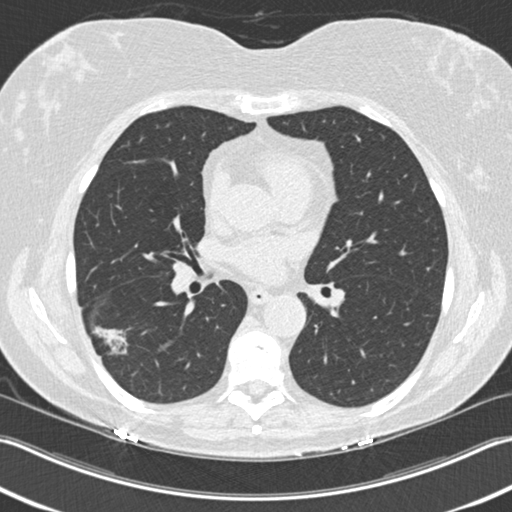
Chest CT (low-dose screening protocol), one axial image, baseline annual screen, lung window (W 1500 / L -600 HU), 2 mm slice thickness, standard (soft-tissue) reconstruction kernel (B30f), 120 kVp, slice 92 of 211 in the series. Female participant, aged 63 years at enrolment. Current smoker at enrolment.
Expert reader's lesion annotation, bounding box <82,317,142,371> (left, top, right, bottom; pixels). The screening reader recorded 3 non-calcified nodules or masses ≥4 mm on this exam (right upper lobe, right lower lobe, right lower lobe); which of them this box marks is not recorded. Official screen result: positive, change unspecified: nodule(s) >= 4 mm or enlarging nodule(s), mass(es), or other non-specific abnormalities suspicious for lung cancer. Later outcome: lung cancer diagnosed 57 days after this screen — bronchiolo-alveolar adenocarcinoma, NOS, right lower lobe, well differentiated (G1), stage IA (AJCC 6th edition), 25 mm at pathology.